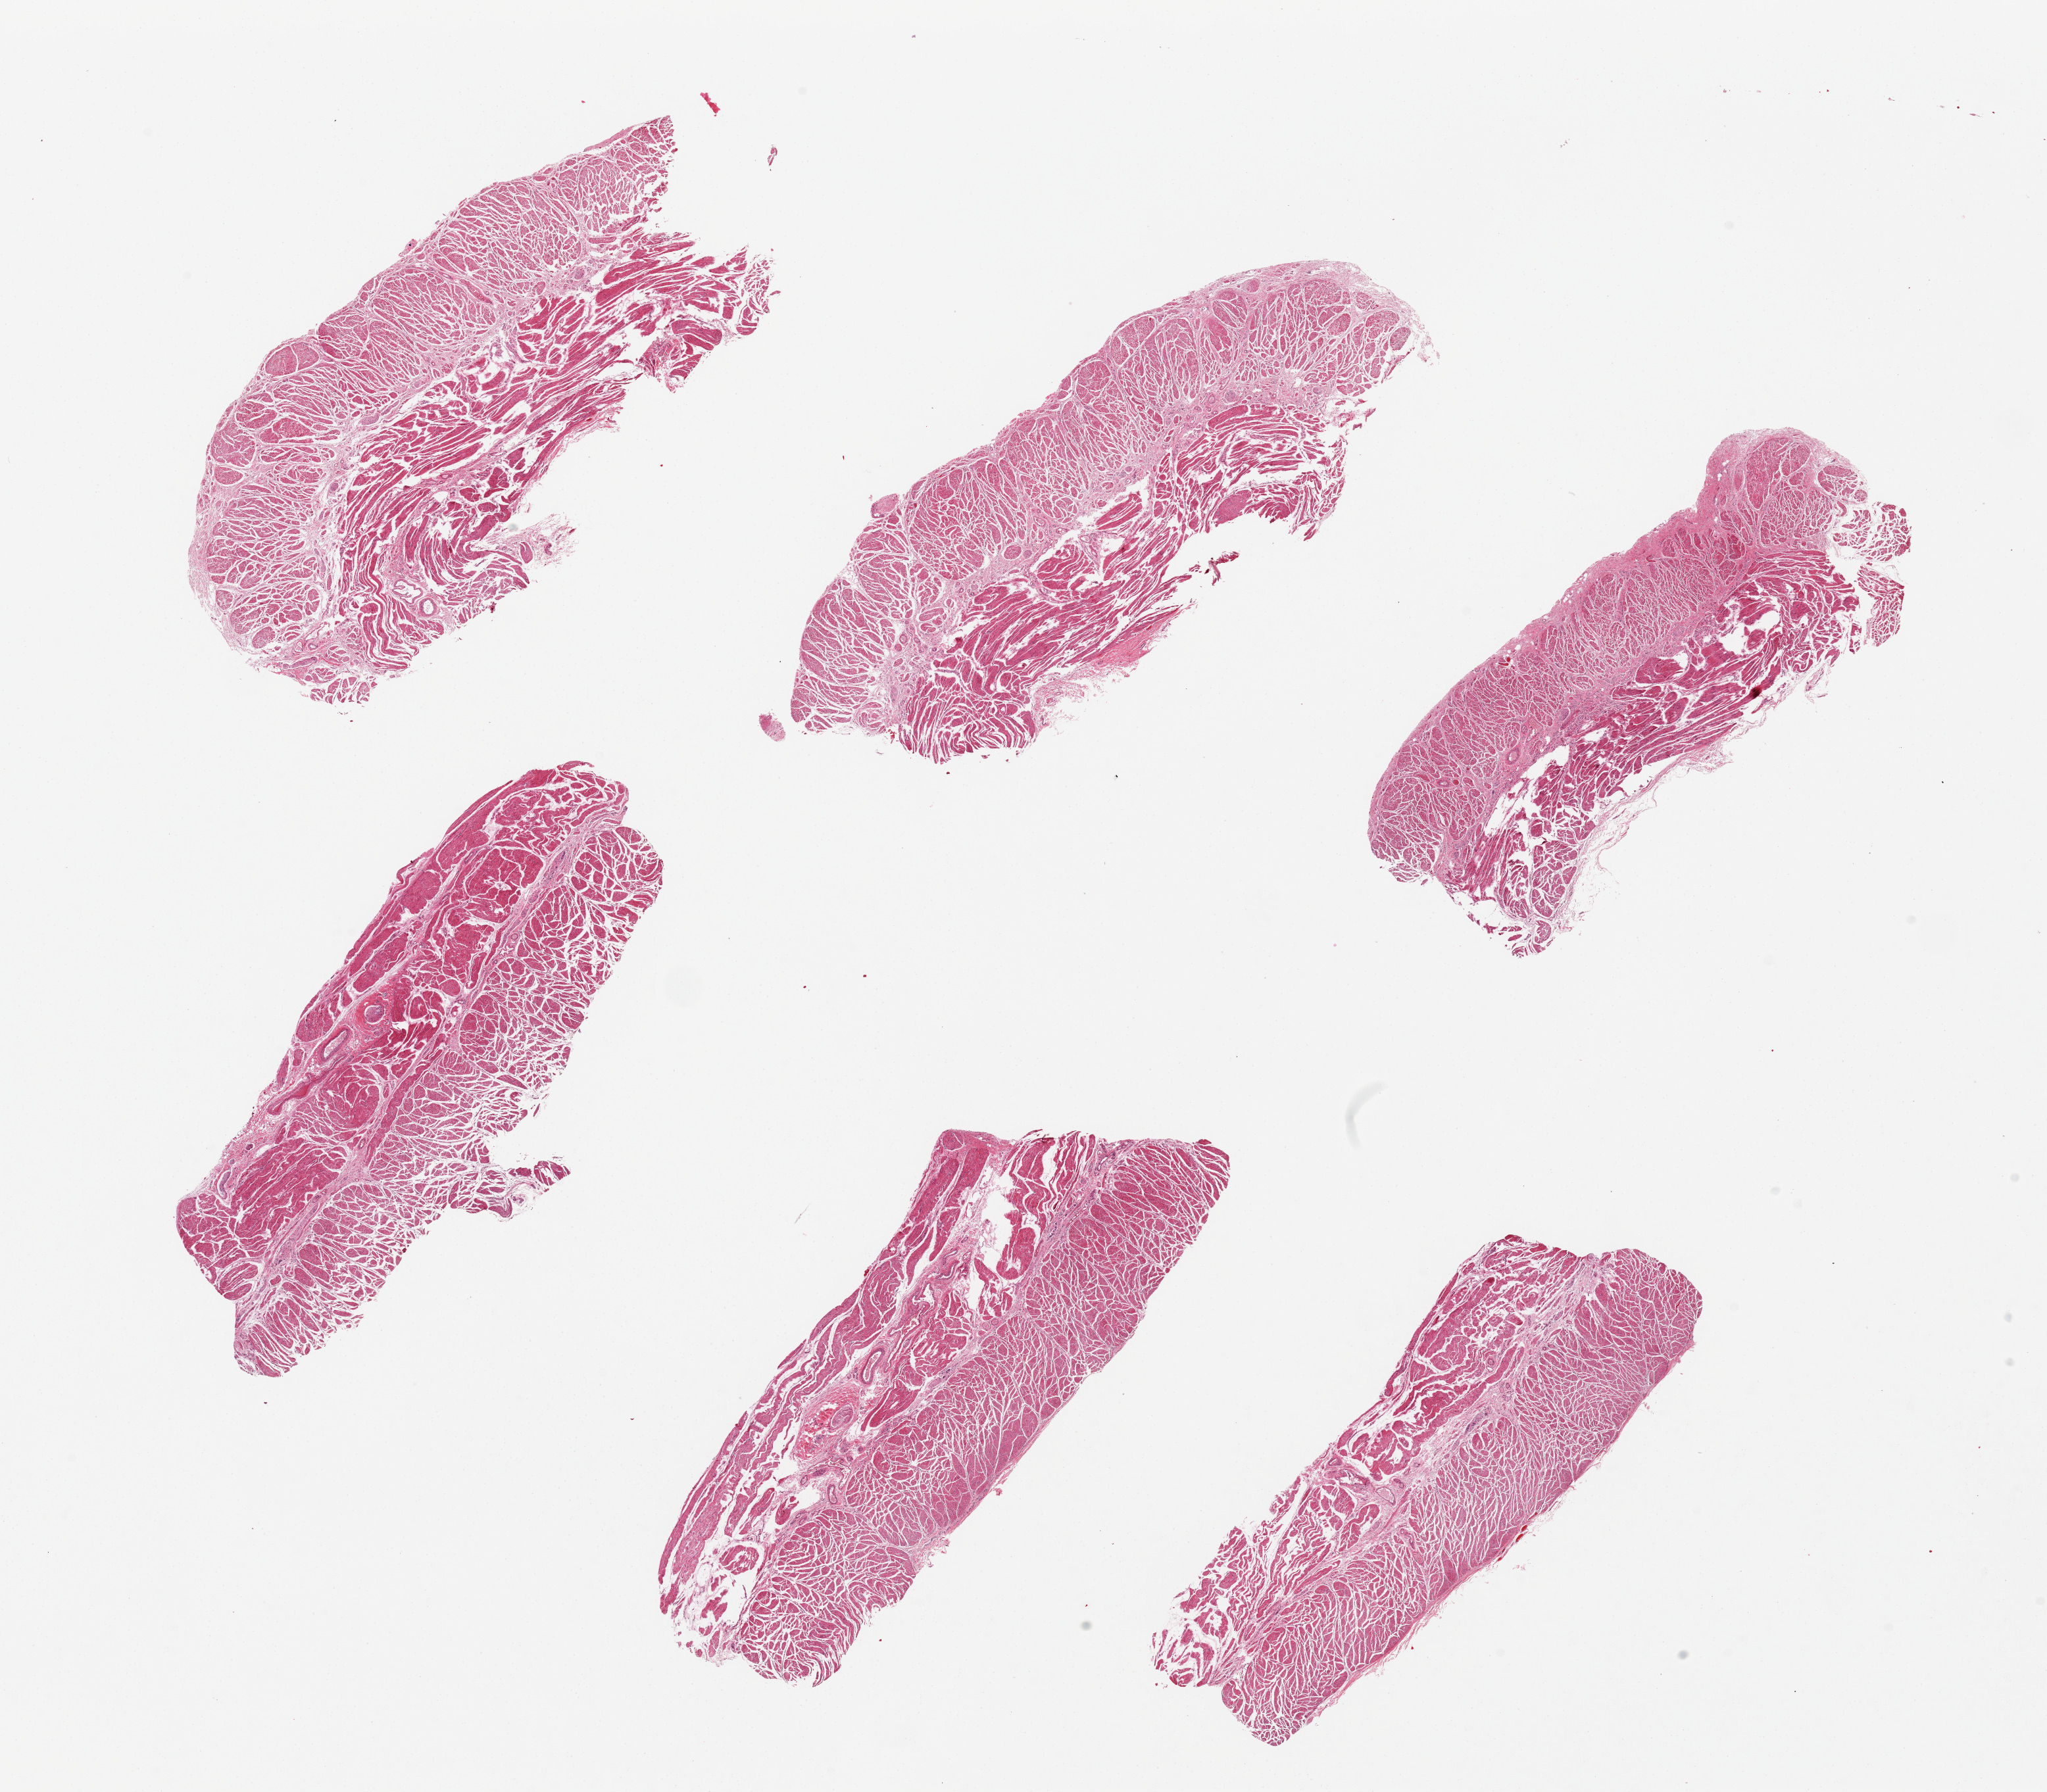
Haematoxylin and eosin whole-slide image — low-resolution overview of the scanned area, about 24.6 x 21.6 mm (acquisition: 20x scan); PAXgene-fixed paraffin-embedded (PFPE) section; section of gastroesophageal junction (target tissue); donor tissue sample. Male donor.
- reviewer comment on this tissue sample: 6 pieces. Well trimmed